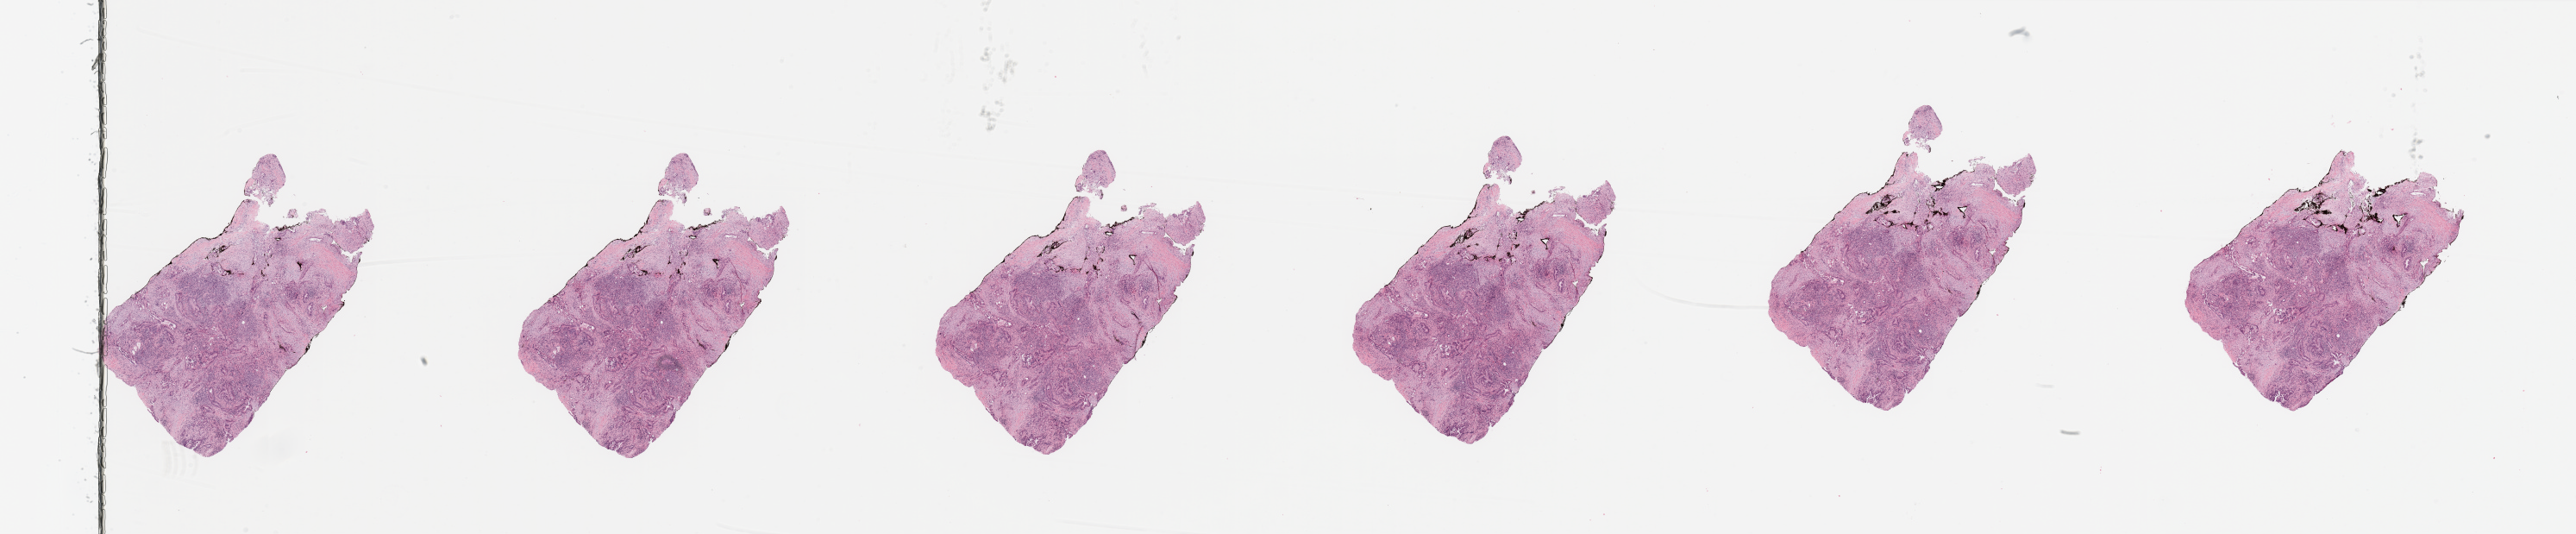
H&E whole-slide image — low-resolution overview of the scanned area, about 47.3 x 9.8 mm (acquisition: 20x scan); tumour tissue sample, sampled site: pancreas. Patient: female, age 69 years. Histologic grade: G2 (moderately differentiated). Composition of this section per pathologist review: tumour nuclei 30%, necrosis 0%.
Diagnosis: Infiltrating duct carcinoma, NOS. AJCC pathologic stage: IIB.